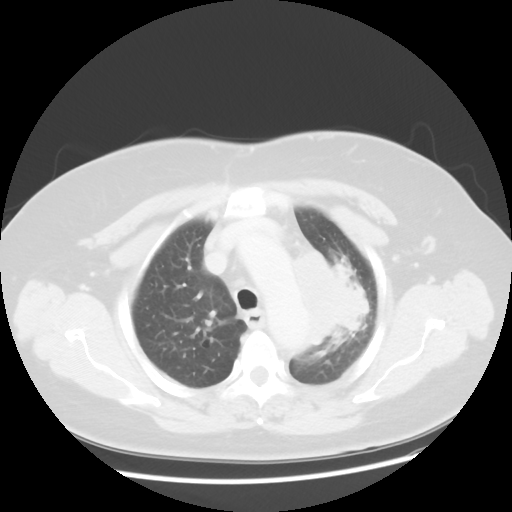
Chest CT, one axial slice. Slice 37 of 49 in the series (ordered by position). Reconstruction kernel STANDARD. 120 kVp. Lung window (W 1500 / L -600 HU). 5 mm slice thickness. 512 × 512 image matrix. Female patient, age 58 years. Case-level facts recorded for this patient, not image findings: clinical TNM (as recorded): T4 N3 M0; histopathological grade: G3.
Outlined on this slice (rectangle marked by the reading radiologist):
- lung tumour (recorded histology: small cell carcinoma): bounding box (x1, y1, x2, y2) in pixels: (289, 242, 378, 352)